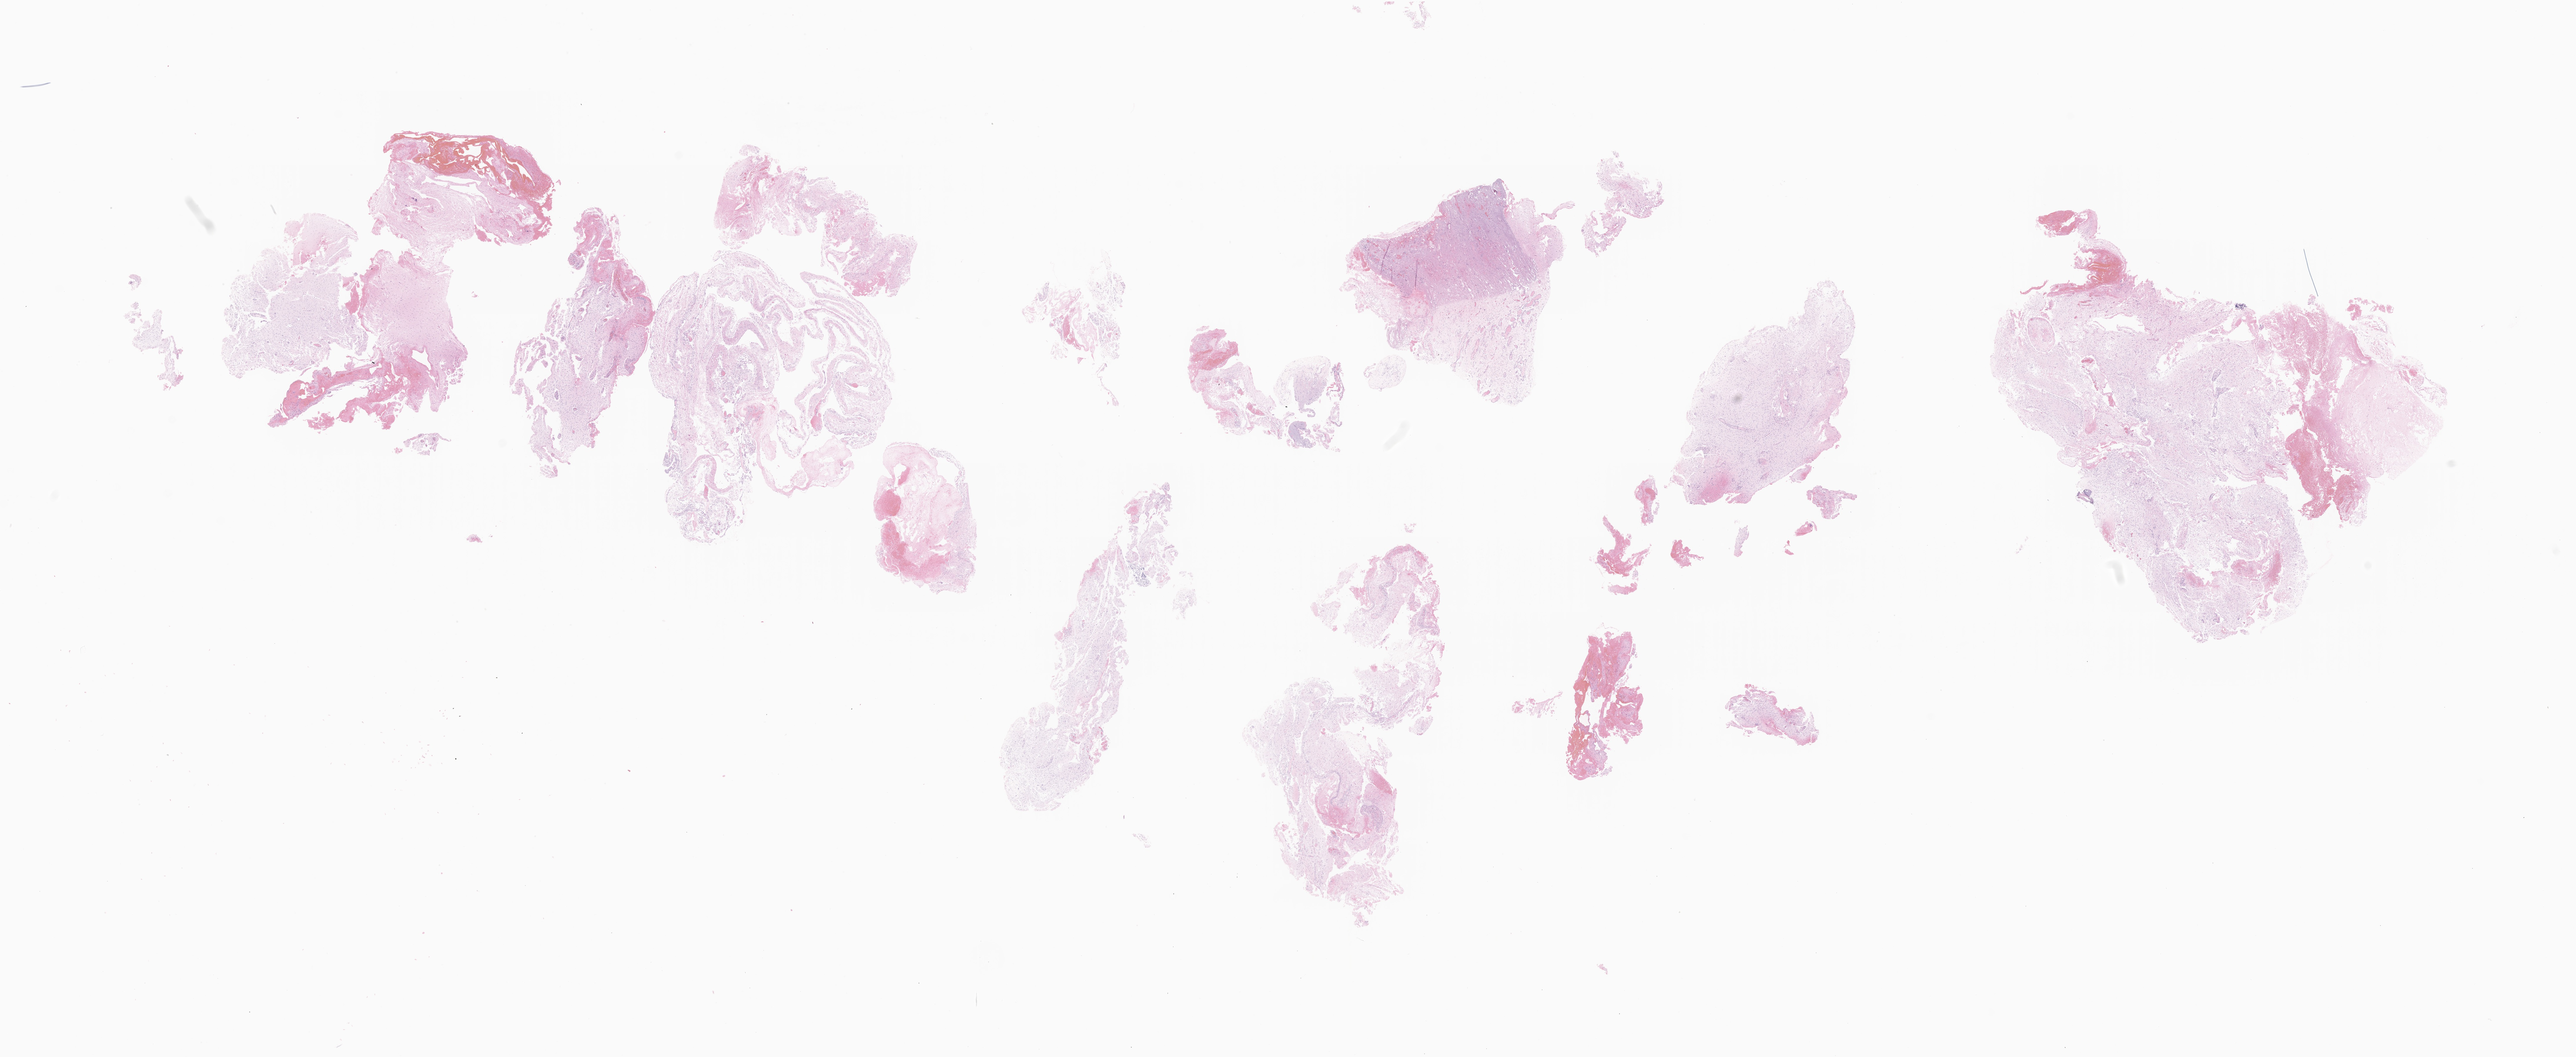
Digitized hematoxylin and eosin (H&E)-stained section of tumor tissue from the brain — a low-resolution overview of the entire scanned area, about 36.9 x 15.2 mm, FFPE section. Female patient, age 104 months.
Diagnosis: Pilocytic astrocytoma.